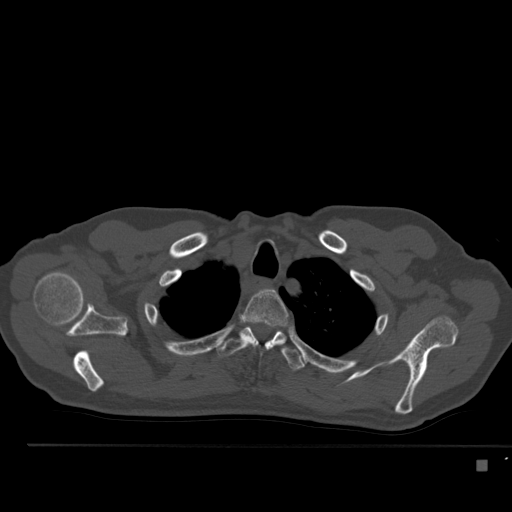
CT including the spine, one axial slice; position 405 of 517 along the scan axis; reconstruction kernel Br40s; bone window (W 1800 / L 400 HU); 1.5 mm slice thickness; 512 × 512 image matrix. Male patient, age 70 years. Case-level facts recorded for this patient, not image findings: primary cancer: renal.
Structures marked on this image (semi-automatically segmented with operator editing):
- T2 vertebra: bounding box [x1, y1, x2, y2] px = [243, 289, 289, 340]
- T3 vertebra: [216, 325, 306, 370]